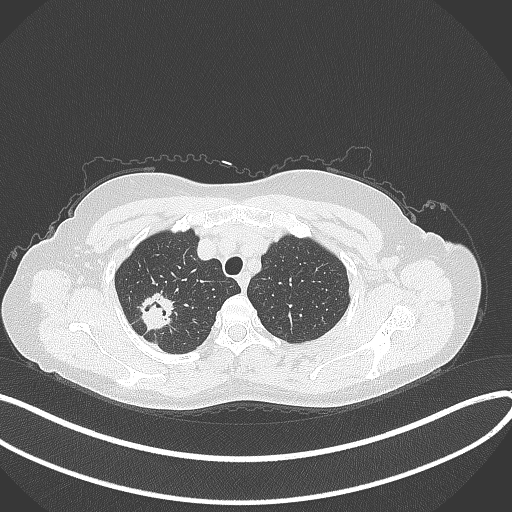
Chest CT, one axial slice. Position 304 of 337 along the scan axis. Reconstruction kernel B70f. 120 kVp. Lung window (W 1500 / L -600 HU). 1 mm slice thickness. 512 × 512 image matrix, field of view 400 × 400 mm. Patient: female, 50 years. From the clinical record (not read from this slice): clinical TNM (as recorded): T1c N0 M0; histopathological grade: G2-3.
Outlined on this slice (rectangle marked by the reading radiologist):
- lung tumour (recorded histology: adenocarcinoma): box from (x=139, y=284) to (x=178, y=335) px